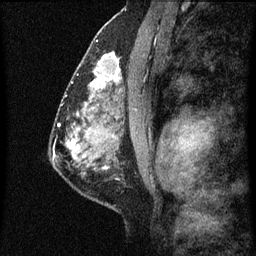
Breast MRI (dynamic contrast-enhanced), one sagittal slice. Slice 38 of 60 in the series (ordered by position). Dynamic contrast-enhanced series, image 2 of 7 at this slice position (ordered by acquisition). 1.5 T. TE 4.2 ms, TR 8 ms. 2 mm slice thickness. 256 × 256 image matrix, field of view 180 × 180 mm. Patient: female, 51 years.
Annotated regions visible in this slice (semi-automatically segmented with operator editing):
- analysis volume of interest (the breast-tissue region the enhancement analysis was run in; not a lesion): bounding box [x1, y1, x2, y2] px = [86, 48, 125, 101]
- tumour enhancement mask (voxels above the 70 % enhancement threshold inside the analysis volume of interest): [93, 54, 121, 97]